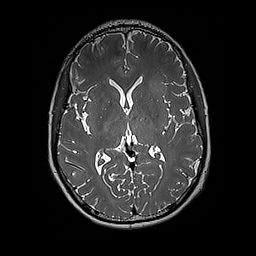
Brain MRI from a brain-tumour surgery series, one axial slice; position 97 of 192 along the scan axis; 1 mm slice thickness; 256 × 256 image matrix, field of view 250 × 250 mm. Case-level facts recorded for this patient, not image findings: histopathology: Glioblastoma; WHO grade: 4; IDH mutation: no.
Outlined on this slice (expert manual segmentation):
- tumour: bounding box [x1, y1, x2, y2] px = [140, 76, 171, 96]